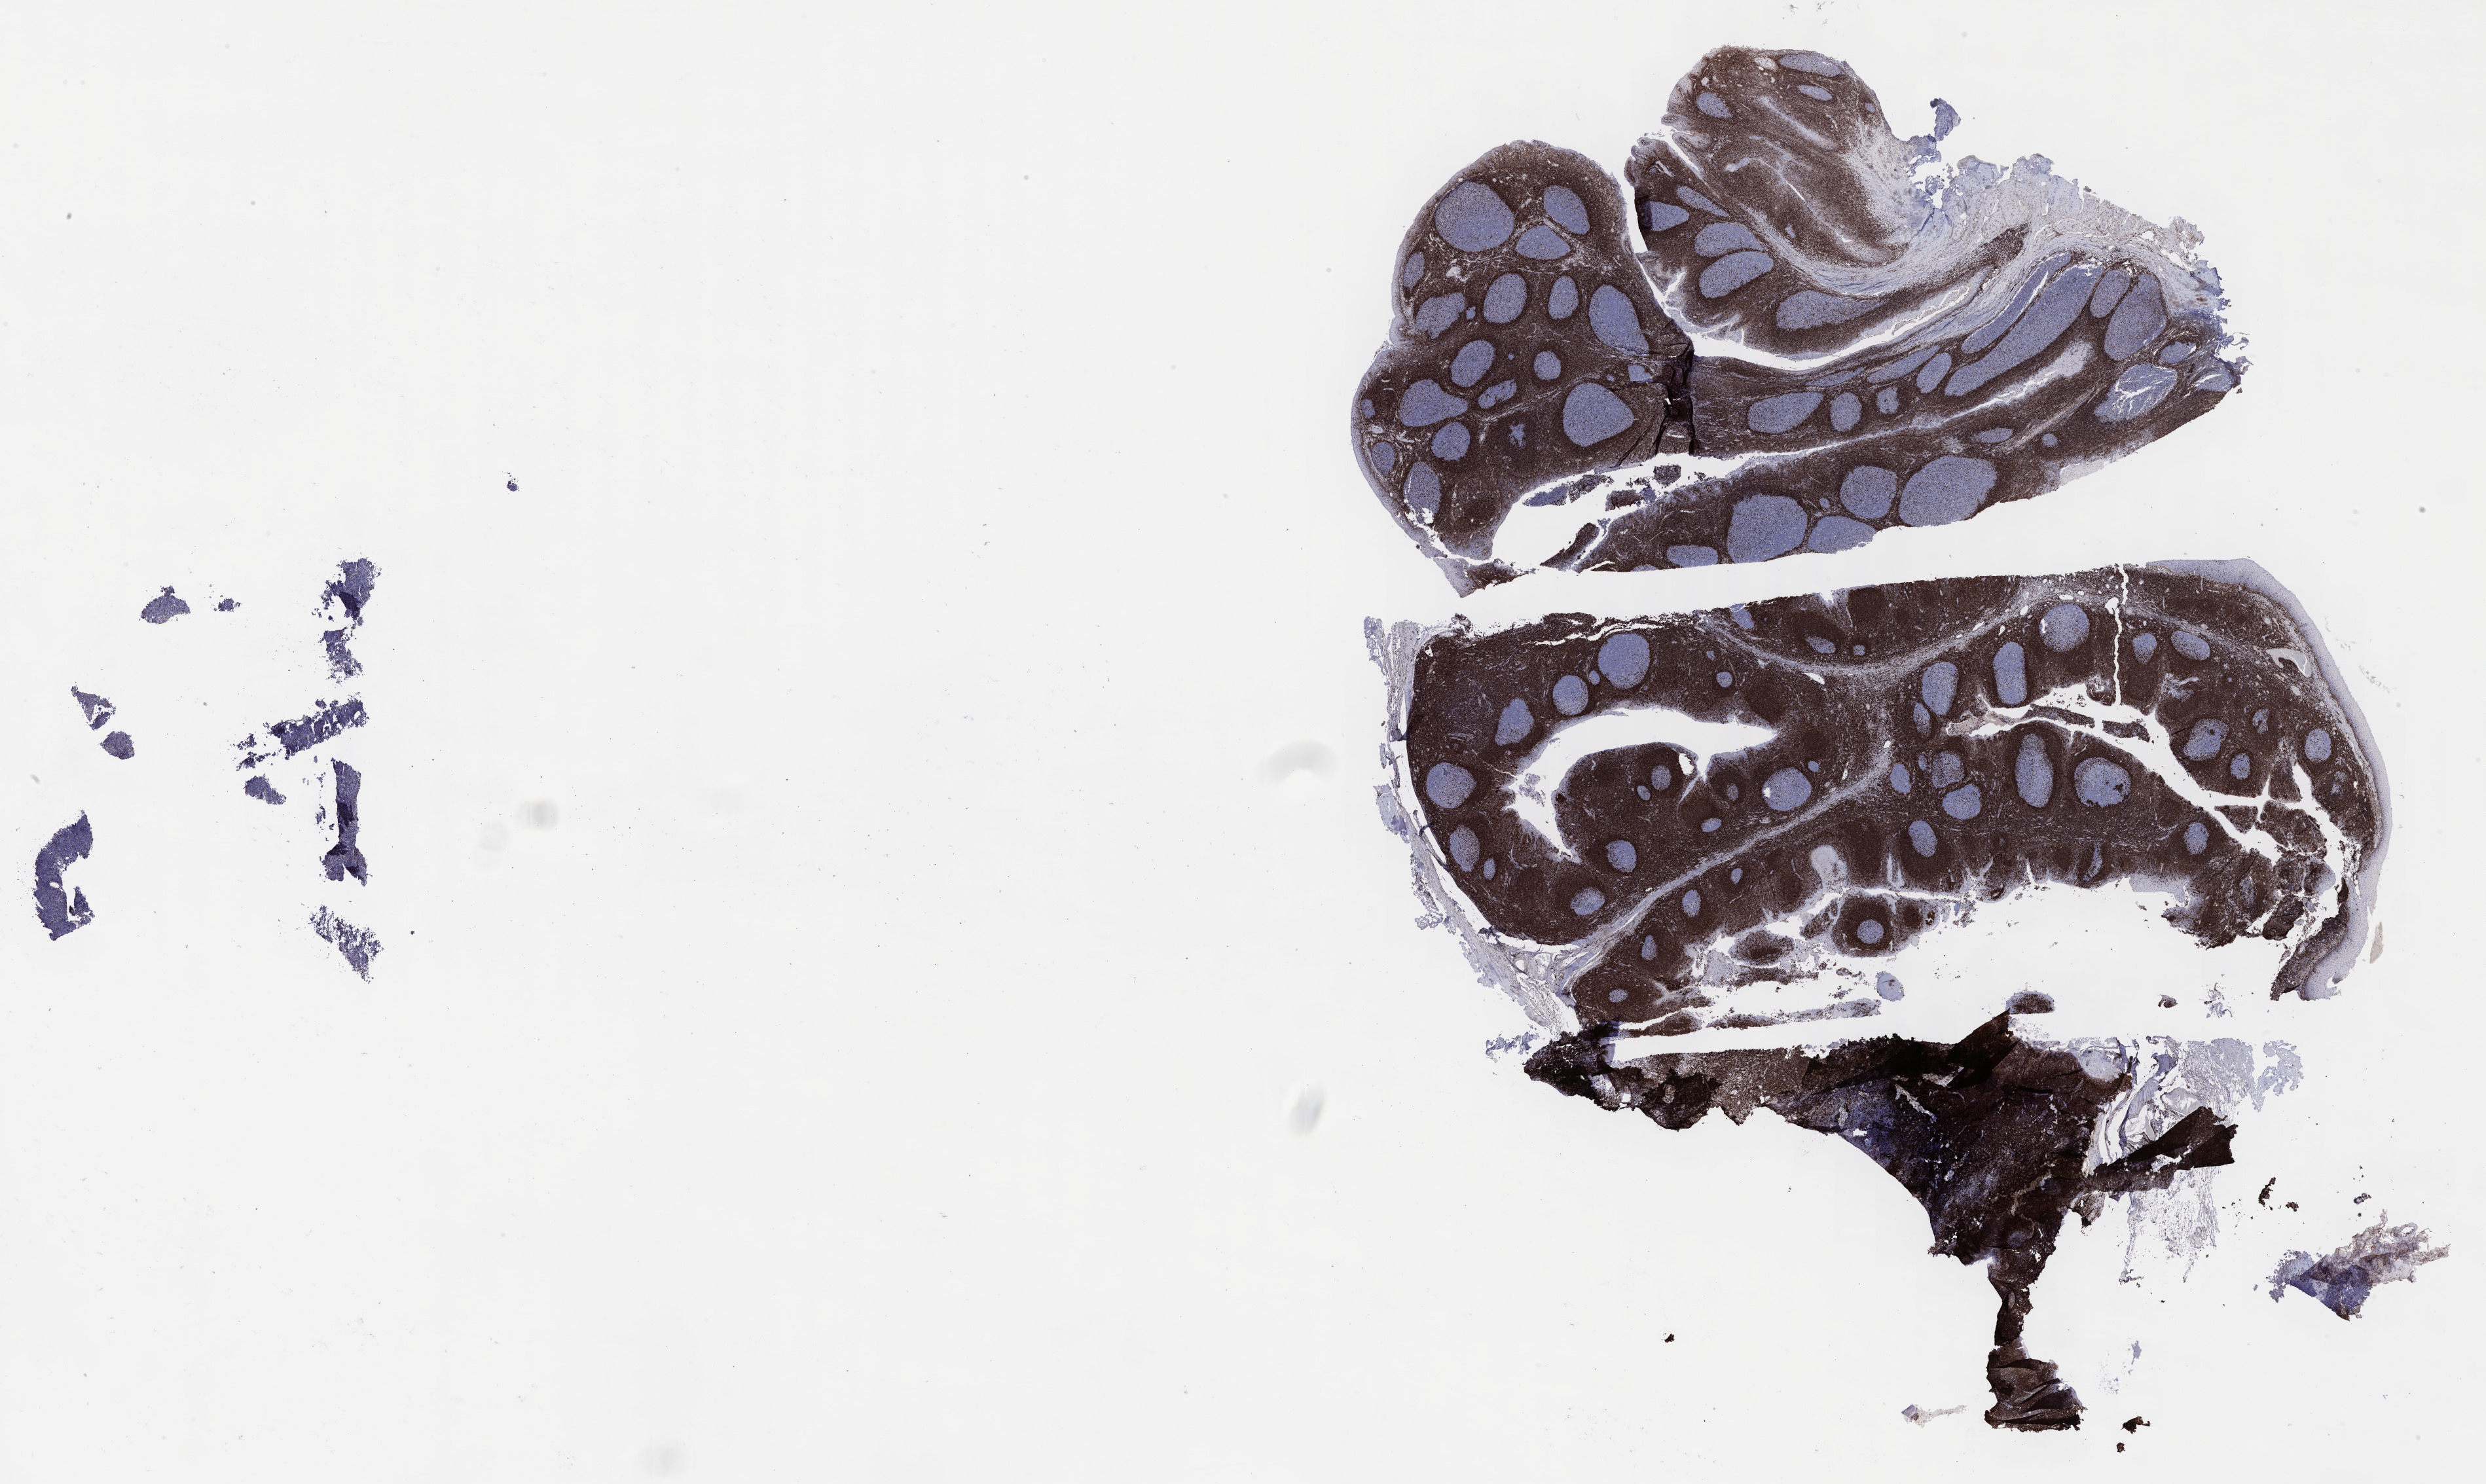
IHC for BCL2, whole-slide image — whole scanned area (about 30.7 x 18.3 mm) shown as a low-resolution overview; tumor tissue; anatomic site: peritoneum. Female patient; age at initial diagnosis 6 years.
Diagnosis: Burkitt lymphoma, NOS.